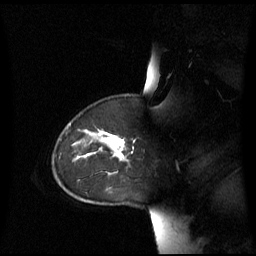
Breast MRI (dynamic contrast-enhanced), one sagittal slice; position 47 of 60 along the scan axis; dynamic contrast-enhanced series, image 2 of 3 at this slice position (ordered by acquisition); 1.5 T; TE 4.2 ms, TR 8.4 ms; 256 × 256 image matrix. Patient: female, 43 years. From the clinical record (not read from this slice): setting: breast cancer imaged before/during neoadjuvant chemotherapy; receptor status: triple-negative.
Annotated regions visible in this slice (semi-automatically segmented with operator editing):
- analysis volume of interest (the breast-tissue region the enhancement analysis was run in; not a lesion): box from (x=55, y=124) to (x=129, y=173) px
- tumour enhancement mask (voxels above the 70 % enhancement threshold inside the analysis volume of interest): (x=104, y=136)–(x=125, y=156)